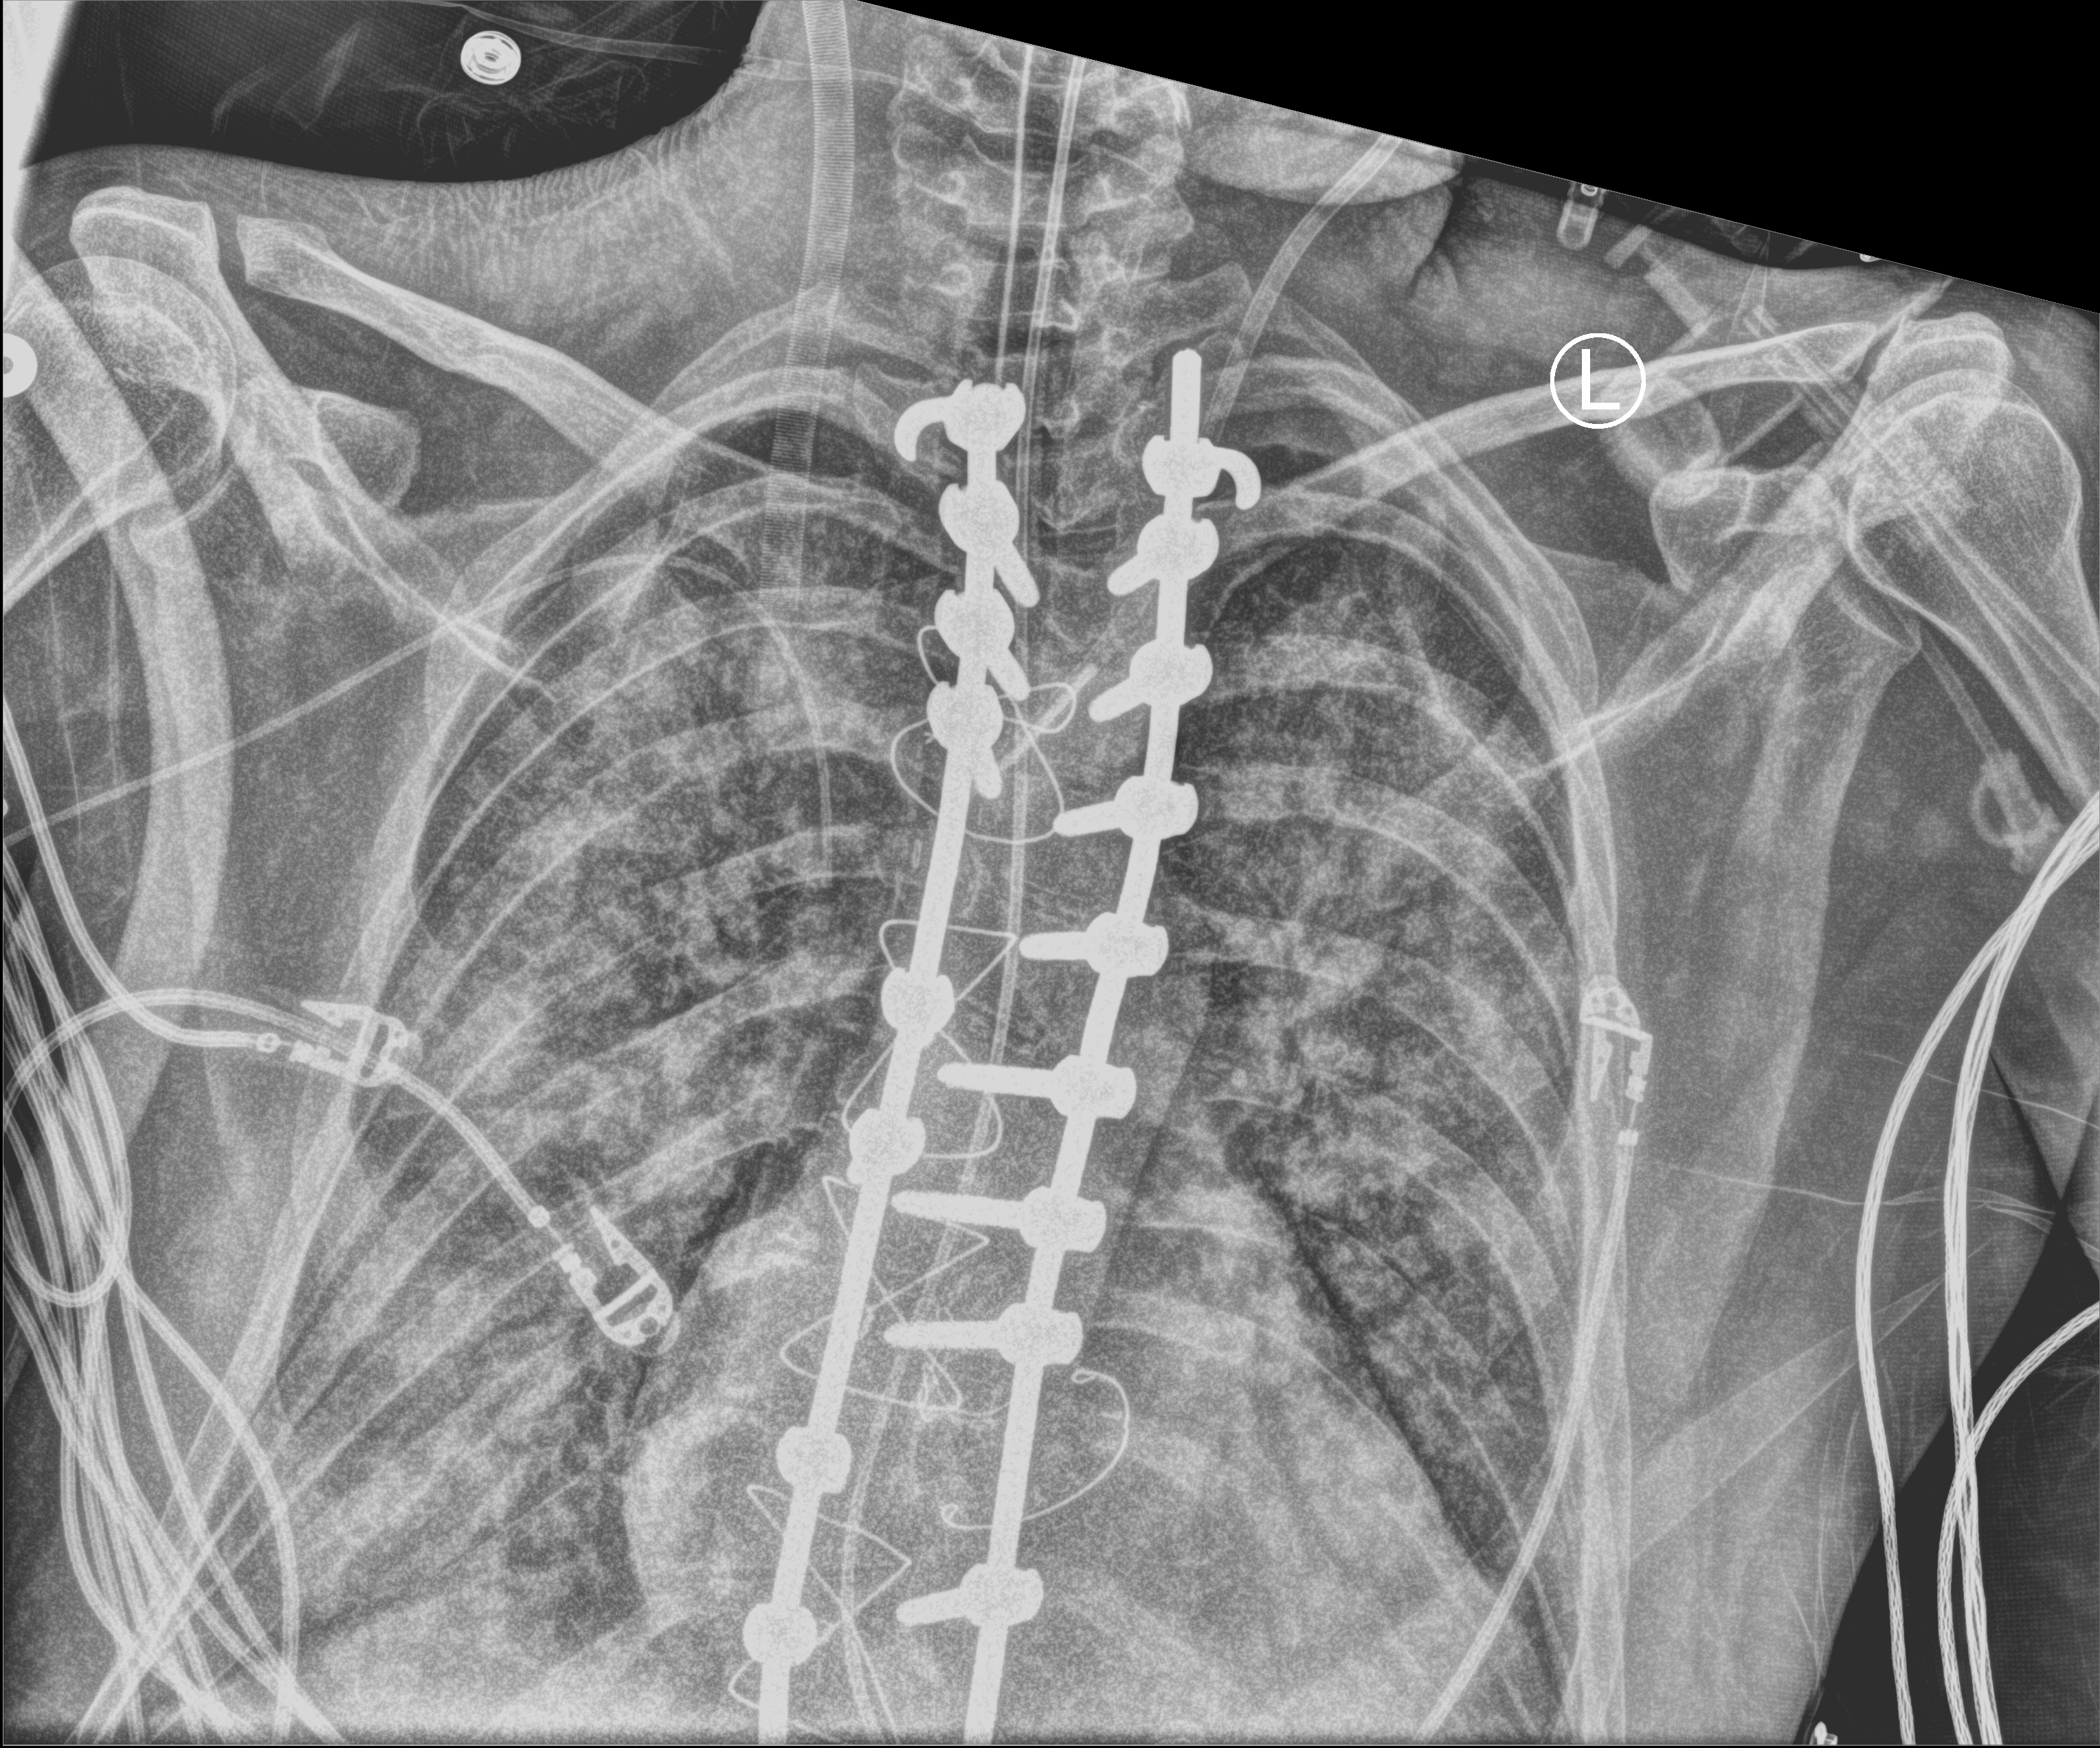
Portable chest radiograph, anteroposterior (AP) projection. Adult patient hospitalised with COVID-19, age 18–59 years.
Hospital-stay facts (about this admission, not read from this image; timing relative to this image not recorded): length of hospital stay: 15 days; admitted to intensive care during this hospital stay: yes; mechanically ventilated during this hospital stay: yes.